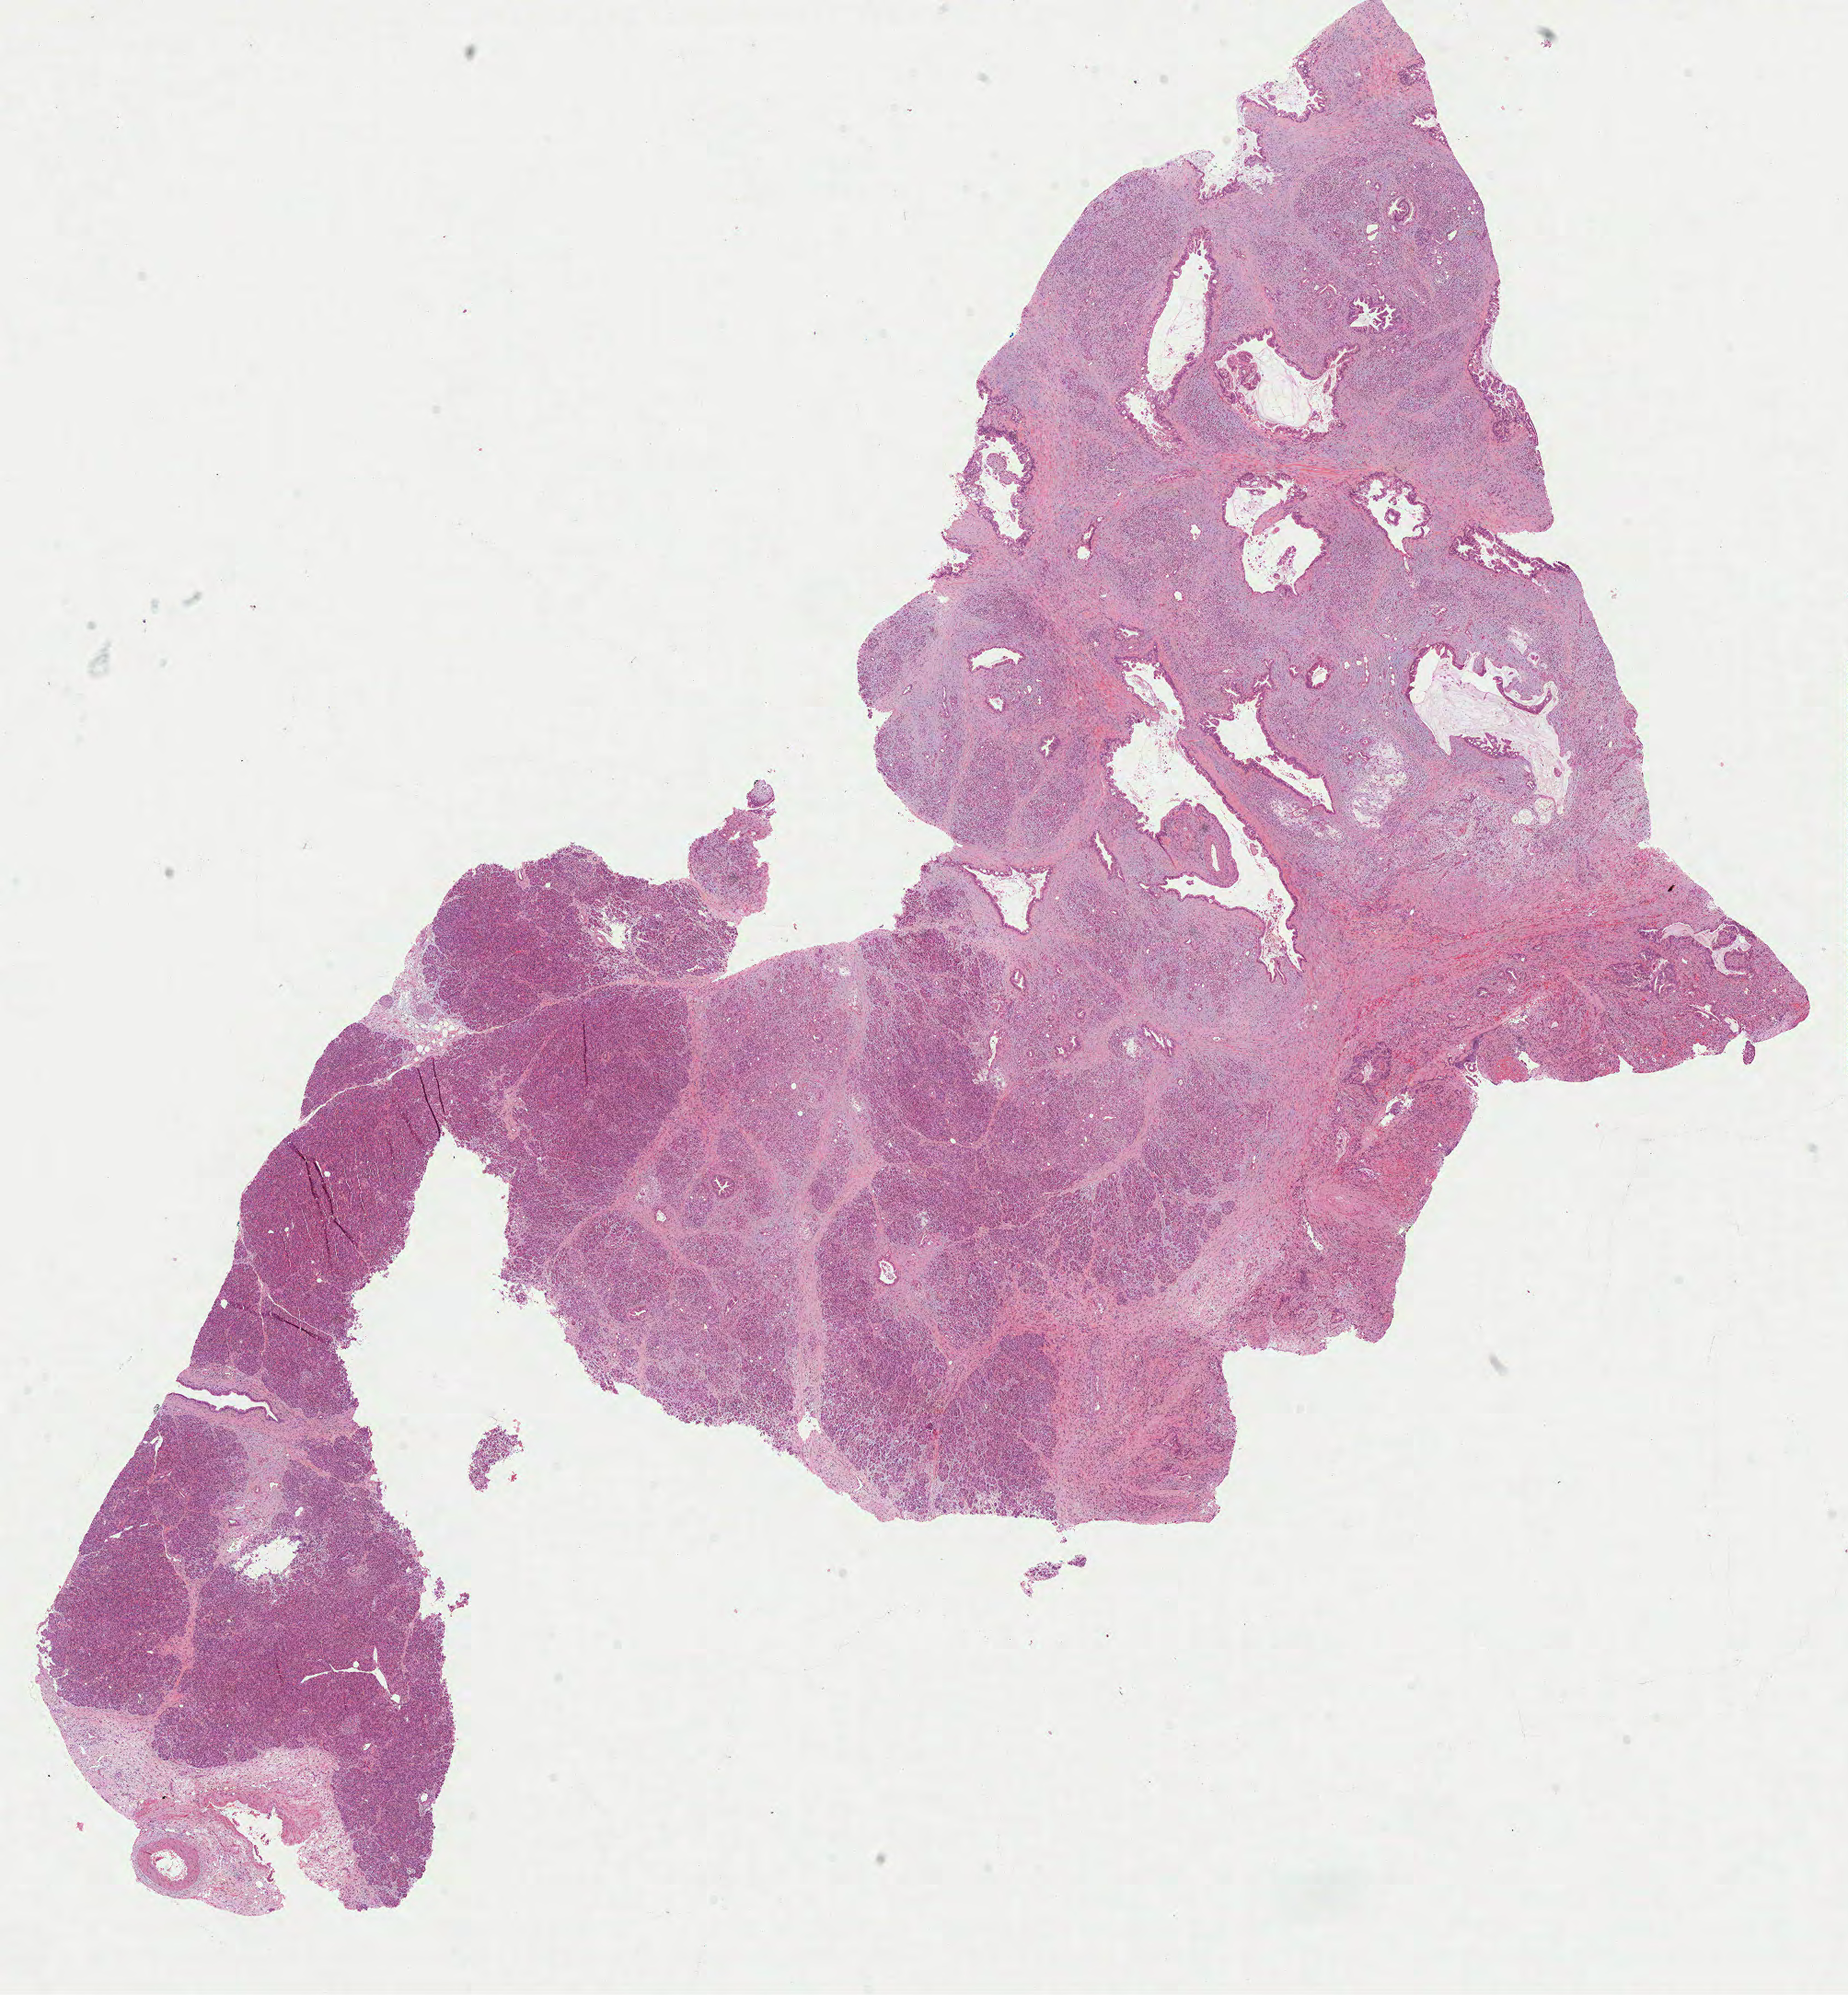
Whole-slide histology image, H&E — whole scanned area (about 16.2 x 17.5 mm) shown as a low-resolution overview; FFPE section; pancreas, primary tumour sample. Female patient; age at initial diagnosis 69 years. Histologic grade: G1 (well differentiated).
• histologic diagnosis: Infiltrating duct carcinoma, NOS
• AJCC pathologic stage: IIB (7th edition)
• lymph nodes positive (case pathology): 4 of 13 examined